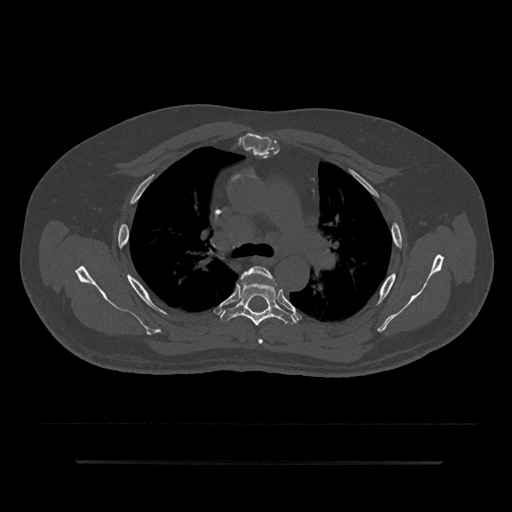
CT including the spine, one axial slice. Slice 583 of 797 in the series (ordered by position). Reconstruction kernel Br40s/3. 120 kVp. Bone window (W 1800 / L 400 HU). 0.5 mm slice thickness. 512 × 512 image matrix, field of view 464 × 464 mm. Patient: male, 59 years. From the clinical record (not read from this slice): primary cancer: bile ducts.
Structures marked on this image (semi-automatic segmentation, software-assisted and operator-edited):
- T4 vertebra: bounding box (x1, y1, x2, y2) in pixels: (241, 266, 277, 344)
- T5 vertebra: (220, 282, 297, 326)